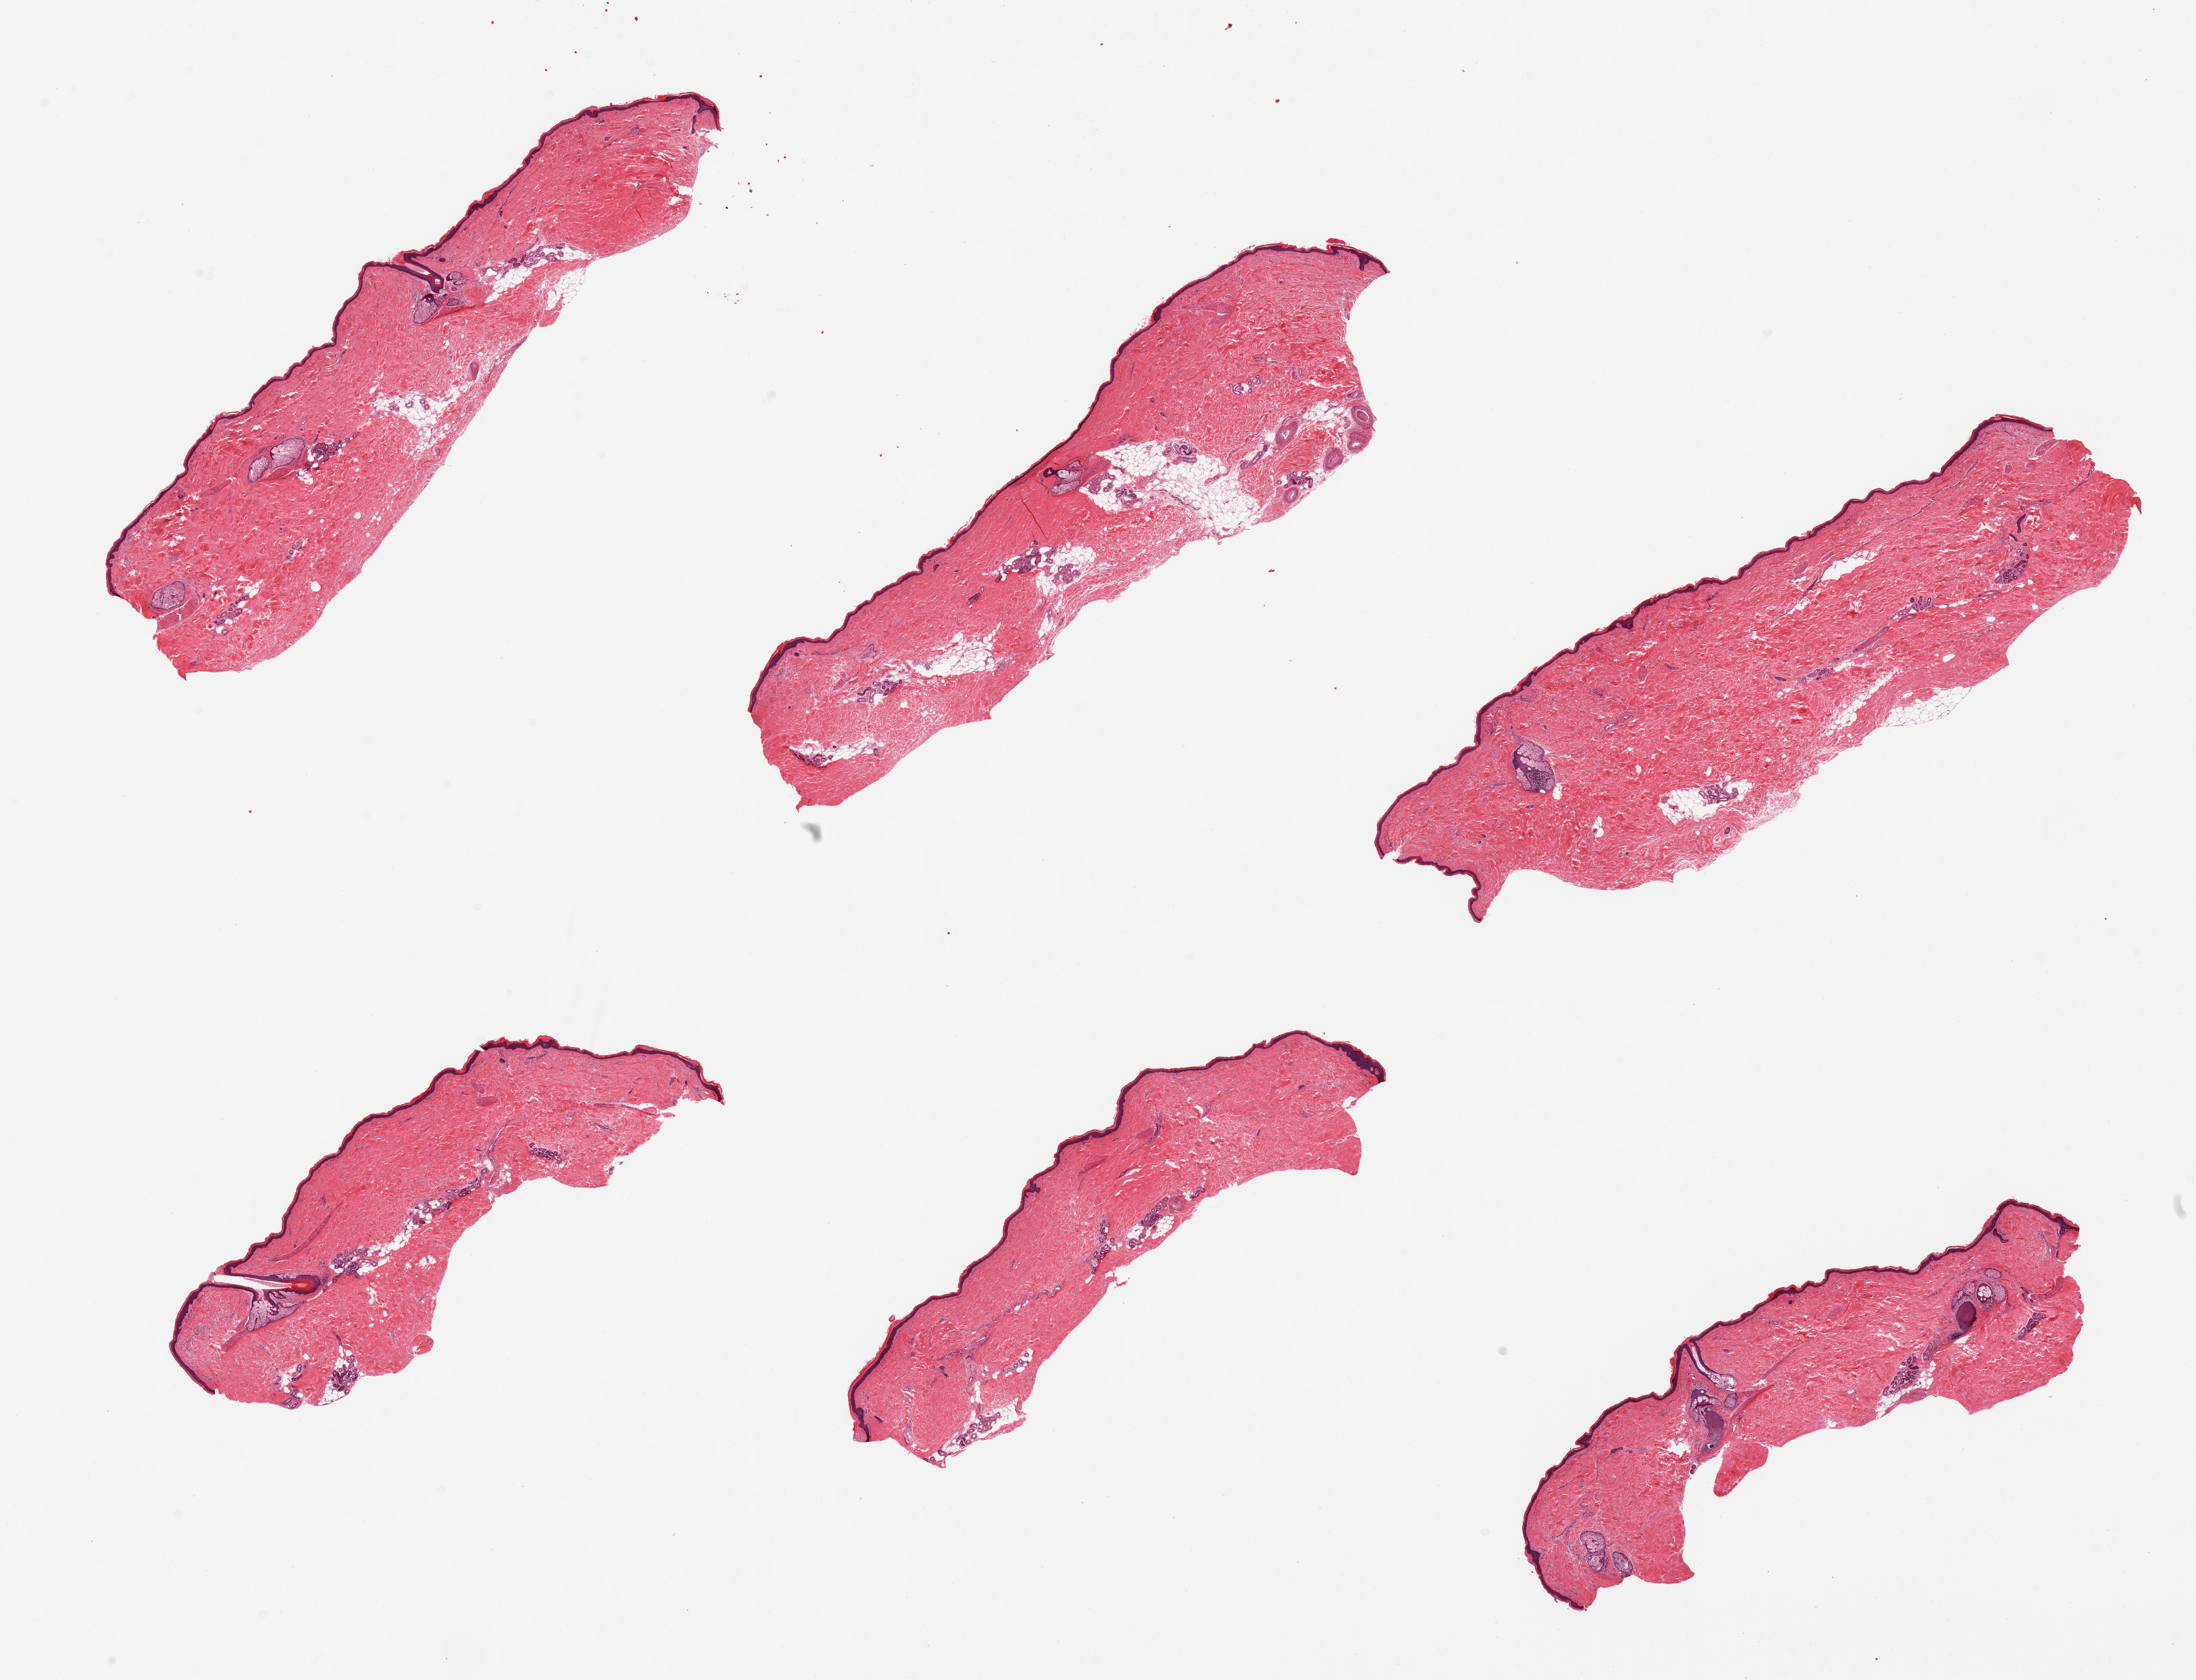
Hematoxylin and eosin (H&E) whole-slide image — shown as a low-resolution overview of the whole scanned area (about 25.6 x 19.6 mm). PAXgene-fixed, paraffin-embedded tissue. Section of skin of lower leg (target tissue). Tissue donor sample. Male donor.
* pathologist's review note for this sample: 6 pieces, no significant dermal fat; squamous epithelium is ~30 microns